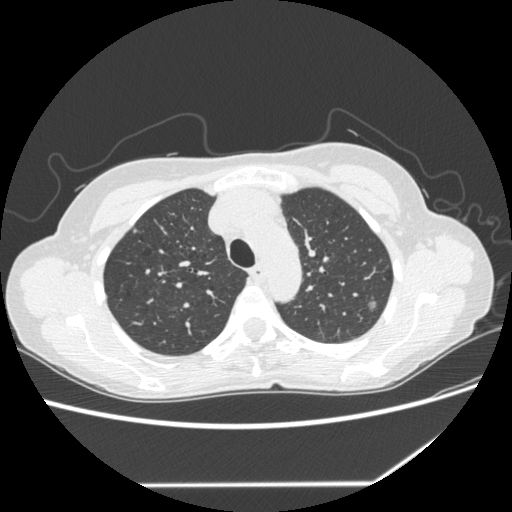
Chest CT (low-dose screening protocol), one axial image; second annual screen; lung window (W 1500 / L -600 HU); 1.25 mm slice thickness; standard (soft-tissue) reconstruction kernel (STANDARD); slice 56 of 255 in the series. Female, age 61 years at enrolment.
• Expert reader's lesion annotation, bounding box <357,293,387,319> (left, top, right, bottom; pixels).
• Screening reader's record for this exam (one nodule recorded; not confirmed to be the boxed lesion): non-calcified nodule or mass ≥4 mm, left upper lobe, 8 × 7 mm, poorly defined margins, mixed attenuation, pre-existing on the prior screen: yes; interval growth: yes.
• Official screen result: positive, change unspecified: nodule(s) >= 4 mm or enlarging nodule(s), mass(es), or other non-specific abnormalities suspicious for lung cancer.
• Participant outcome: lung cancer diagnosed 113 days after this screen — bronchiolo-alveolar adenocarcinoma, NOS, left upper lobe, well differentiated (G1), stage IA (AJCC 6th edition), 8 mm at pathology.